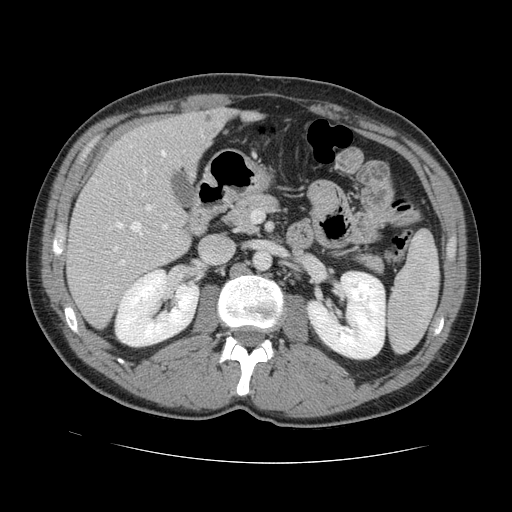
Contrast-enhanced abdominal CT, one axial slice. Position 66 of 131 along the scan axis. 120 kVp. Intravenous contrast given. Soft-tissue window (W 400 / L 40 HU). 2.5 mm slice thickness. 512 × 512 image matrix. Male patient, age 40 years. Case-level facts recorded for this patient, not image findings: diagnosis: colorectal cancer liver metastases, imaged before liver resection; multiple liver metastases: yes; largest metastasis: 2.9 cm; disease in both lobes: yes.
Structures marked on this image (expert manual segmentation):
- hepatic veins: bounding box [x1, y1, x2, y2] px = [114, 145, 167, 251]
- liver: [68, 110, 230, 328]
- planned liver remnant (the part of the liver to remain after resection): [109, 110, 229, 184]
- portal vein (with intrahepatic branches): [120, 169, 168, 265]
- liver metastasis: [206, 115, 213, 122]